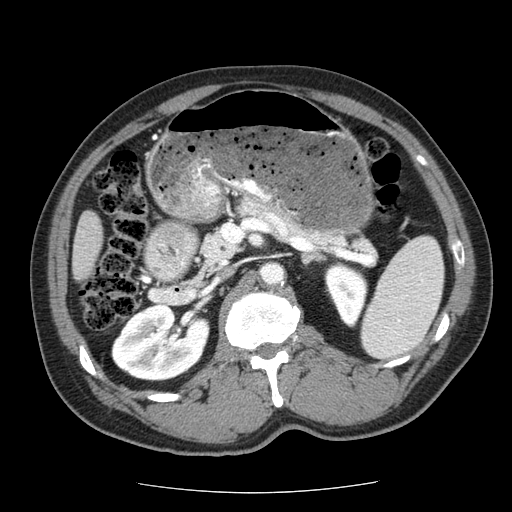
Contrast-enhanced abdominal CT (liver protocol), one axial slice. Position 14 of 85 along the scan axis. Reconstruction kernel STANDARD. 120 kVp. Soft-tissue window (W 400 / L 40 HU). 2.5 mm slice thickness. 512 × 512 image matrix, field of view 360 × 360 mm. From the clinical record (not read from this slice): diagnosis: hepatocellular carcinoma (patient treated with transarterial chemoembolisation; whether this scan precedes or follows treatment is not stated here); TNM stage (as recorded): Stage-IIIA; Child-Pugh class: A; tumour differentiation: well differentiated; tumour size: 8 cm.
Structures marked on this image (semi-automatic segmentation, software-assisted and operator-edited):
- liver parenchyma outside the tumour (the mass and vessels are separate outlines, so this box may not span the whole liver): bounding box (x1, y1, x2, y2) in pixels: (72, 210, 102, 282)